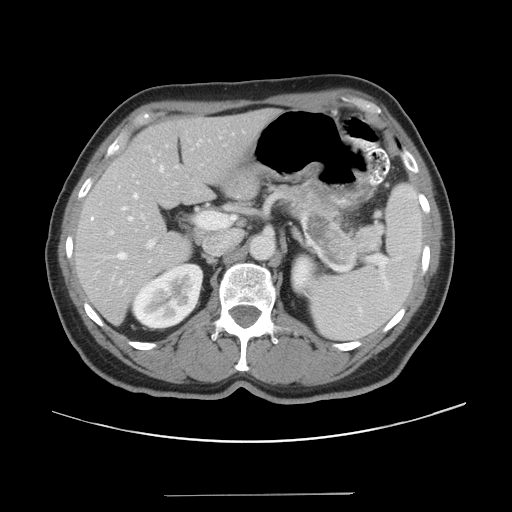
Contrast-enhanced abdominal CT, one axial slice. Position 23 of 43 along the scan axis. 120 kVp. Soft-tissue window (W 400 / L 40 HU). 5 mm slice thickness. 512 × 512 image matrix. Male patient, age 65 years. From the clinical record (not read from this slice): diagnosis: colorectal cancer liver metastases, imaged before liver resection; multiple liver metastases: no.
Outlined on this slice (expert manual segmentation):
- hepatic veins: bounding box [x1, y1, x2, y2] px = [118, 165, 164, 263]
- liver: [75, 109, 276, 321]
- planned liver remnant (the part of the liver to remain after resection): [75, 109, 276, 321]
- portal vein (with intrahepatic branches): [109, 159, 157, 248]